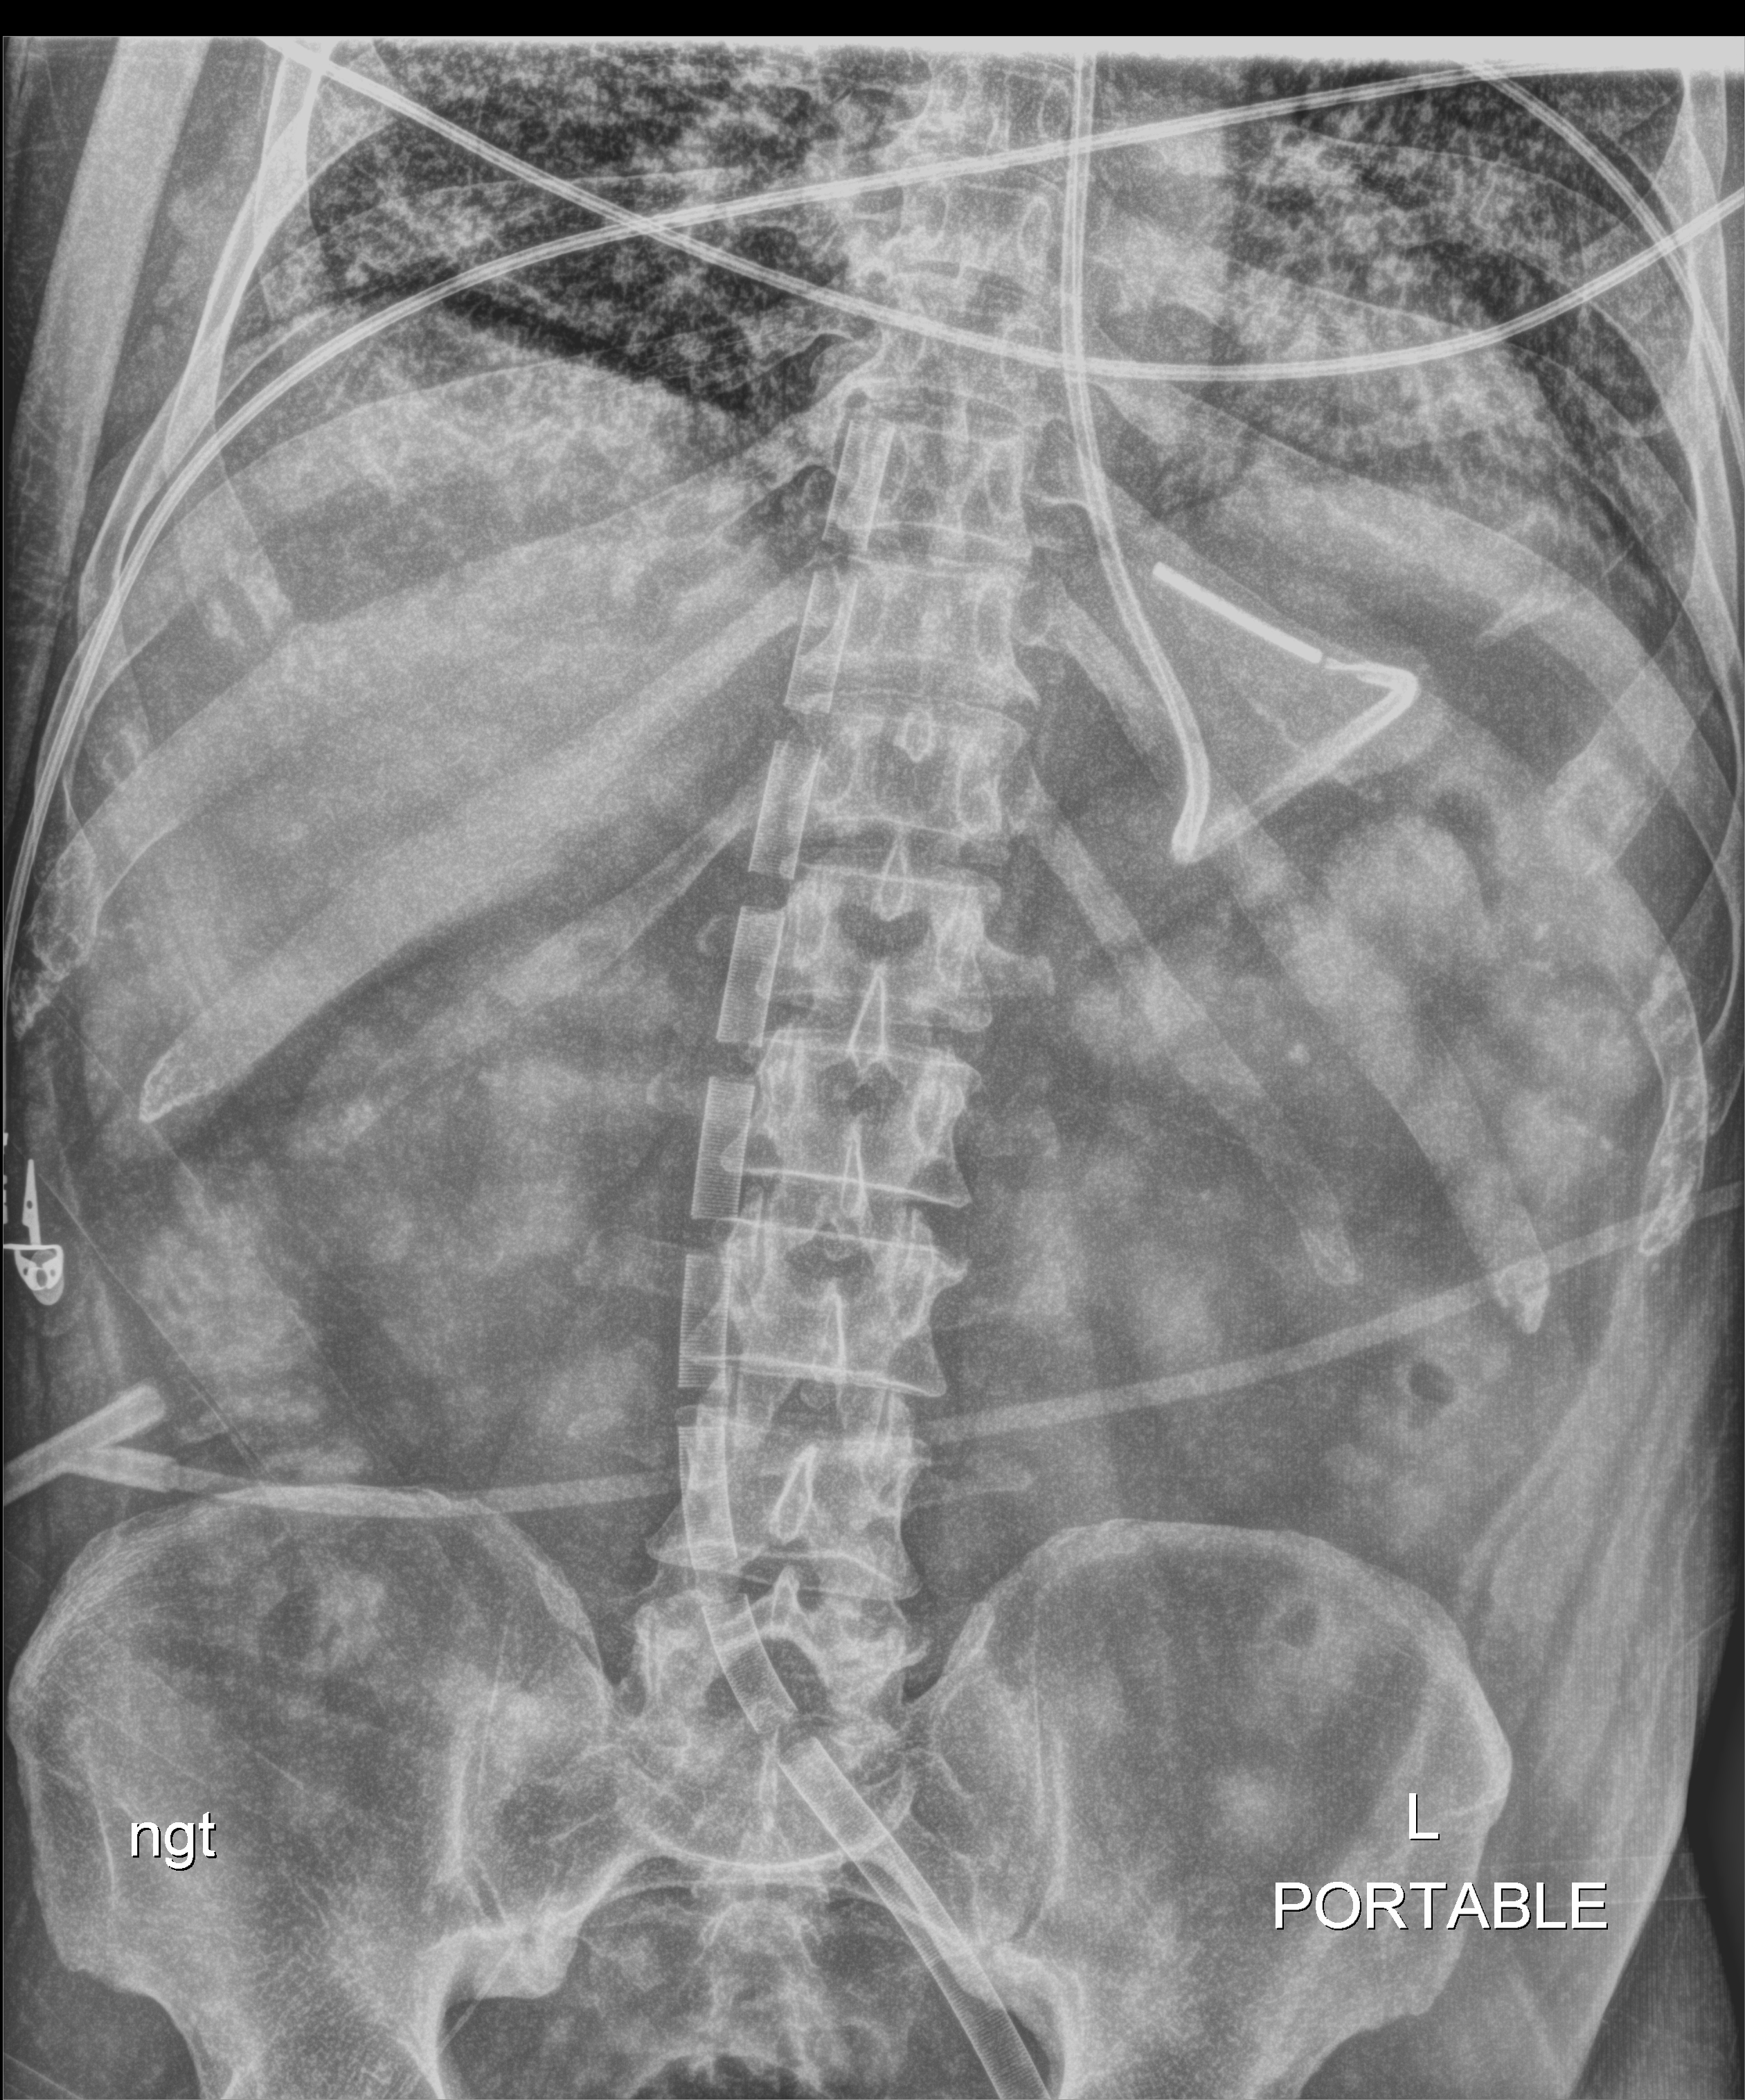
Abdomen X-ray (portable); anteroposterior (AP) projection. Male patient hospitalised with COVID-19, age 18–59 years.
Admission-level facts for this patient (not findings on this image; timing relative to this image not recorded): other chronic lung disease (admission record): no; diabetes (admission record): no.